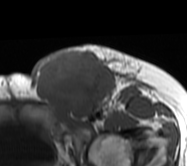
MRI of an extremity soft-tissue mass, one axial slice; MR volume resampled by the dataset authors to the PET/CT grid (not the native acquisition matrix); 3.27 mm slice thickness; 187 × 166 image matrix, field of view 183 × 162 mm. Female patient. From the clinical record (not read from this slice): histological type: leiomyosarcoma; grade: high; site of the primary tumour: groin.
Structures marked on this image (expert contour drawn on MRI and transferred to this co-registered scan by the dataset authors):
- gross tumour volume including surrounding oedema: bounding box (x1, y1, x2, y2) in pixels: (30, 44, 152, 121)
- gross tumour volume (mass): (32, 46, 115, 120)